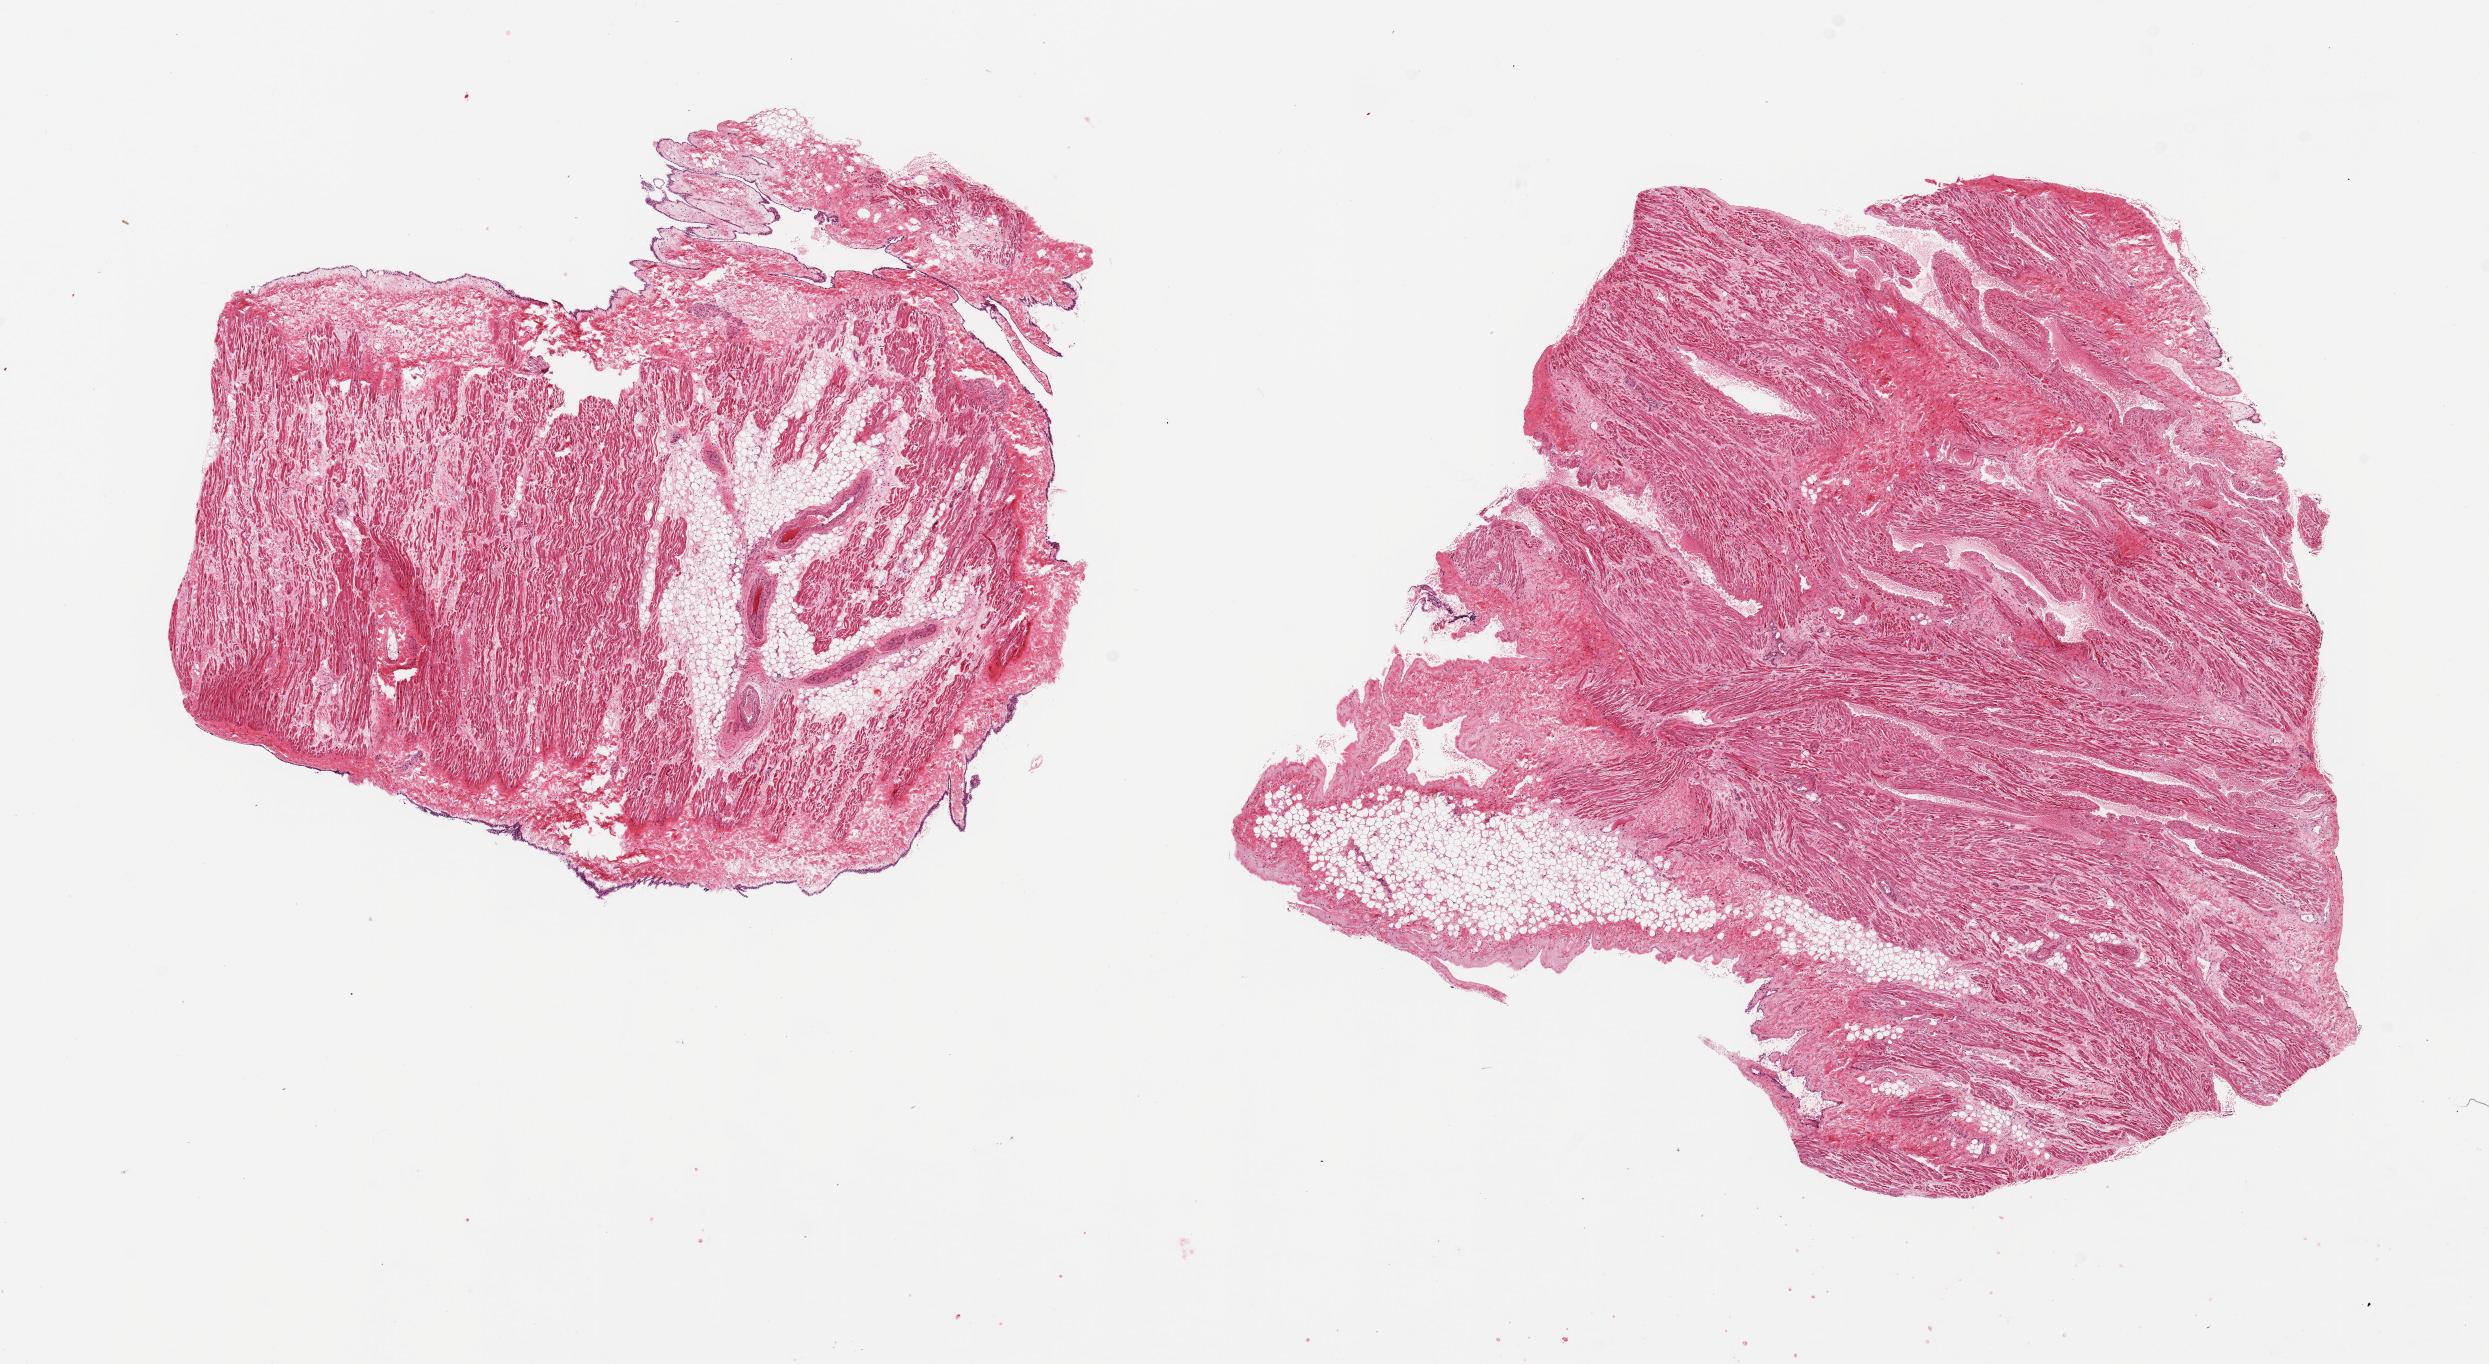
Whole-slide image, H&E stain, low-resolution overview of the scanned area, about 19.7 x 10.8 mm (slide scanned at 20x). PAXgene-fixed paraffin-embedded (PFPE) section. Sampled site (target tissue): auricular appendage. Tissue donor sample. Donor: female.
Review note (as recorded): 2 pieces; 30% fibrofatty internal content.